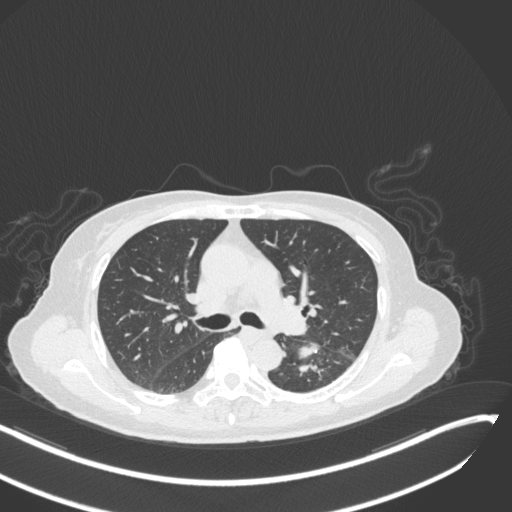
Chest CT, one axial slice; position 178 of 342 along the scan axis; reconstruction kernel B31f; 120 kVp; lung window (W 1500 / L -600 HU); 1 mm slice thickness; 512 × 512 image matrix, field of view 400 × 400 mm. Female patient, age 64 years. From the clinical record (not read from this slice): clinical TNM (as recorded): T3 N1 M1; histopathological grade: G3.
Structures marked on this image (bounding box drawn by a radiologist):
- lung tumour (recorded histology: small cell carcinoma): box from (x=291, y=336) to (x=323, y=363) px